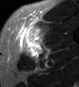
MRI of an extremity soft-tissue mass, one axial slice; position 32 of 45 along the scan axis; STIR; MR volume resampled by the dataset authors to the PET/CT grid (not the native acquisition matrix); 3.27 mm slice thickness; 79 × 87 image matrix. Male patient. Case-level facts recorded for this patient, not image findings: histological type: pleiomorphic leiomyosarcoma; grade: high; site of the primary tumour: left thigh.
Outlined on this slice (expert contour drawn on MRI and transferred to this co-registered scan by the dataset authors):
- gross tumour volume including surrounding oedema: bounding box <20,23,46,58> (left, top, right, bottom; pixels)
- gross tumour volume (mass): <25,34,42,58>